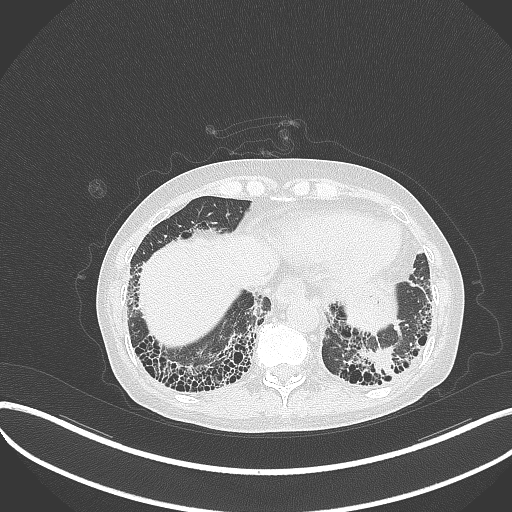
Chest CT, one axial slice; reconstruction kernel B70f; lung window (W 1500 / L -600 HU); 512 × 512 image matrix. Female patient, age 56 years. From the clinical record (not read from this slice): clinical TNM (as recorded): T1 N0 M0.
Structures marked on this image (bounding box drawn by a radiologist):
- lung tumour (recorded histology: adenocarcinoma): bounding box [x1, y1, x2, y2] px = [354, 343, 403, 384]